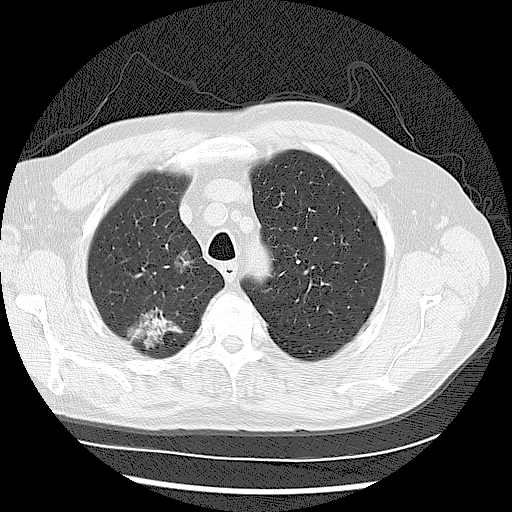
Low-dose screening chest CT, one axial slice; slice 94 of 122 in the series (ordered by position); 120 kVp; lung window (W 1500 / L -600 HU); 512 × 512 image matrix, field of view 360 × 360 mm.
Structures marked on this image (expert manual segmentation):
- lesion 1 (tumor, upper lobe of right lung): bounding box [x1, y1, x2, y2] px = [128, 309, 182, 348]